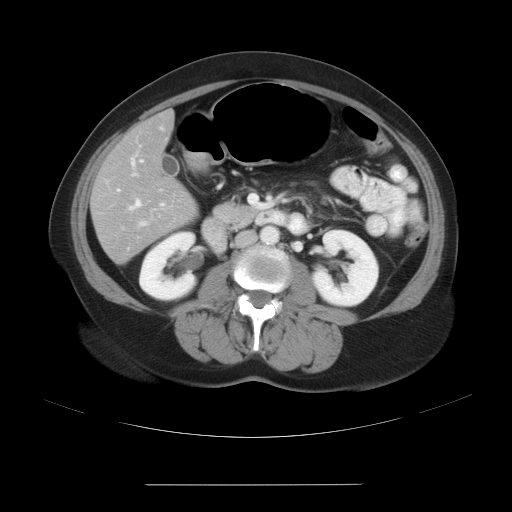
Contrast-enhanced abdominal CT, one axial slice. Slice 10 of 27 in the series (ordered by position). Reconstruction kernel STANDARD. Intravenous contrast given. Soft-tissue window (W 400 / L 40 HU). 7.5 mm slice thickness. 512 × 512 image matrix. Female patient, age 58 years. Case-level facts recorded for this patient, not image findings: diagnosis: colorectal cancer liver metastases, imaged before liver resection; multiple liver metastases: yes.
Outlined on this slice (outlined manually by an expert reader):
- hepatic veins: bounding box (x1, y1, x2, y2) in pixels: (130, 200, 141, 210)
- liver: (92, 112, 196, 262)
- planned liver remnant (the part of the liver to remain after resection): (94, 112, 189, 199)
- portal vein (with intrahepatic branches): (117, 137, 165, 226)